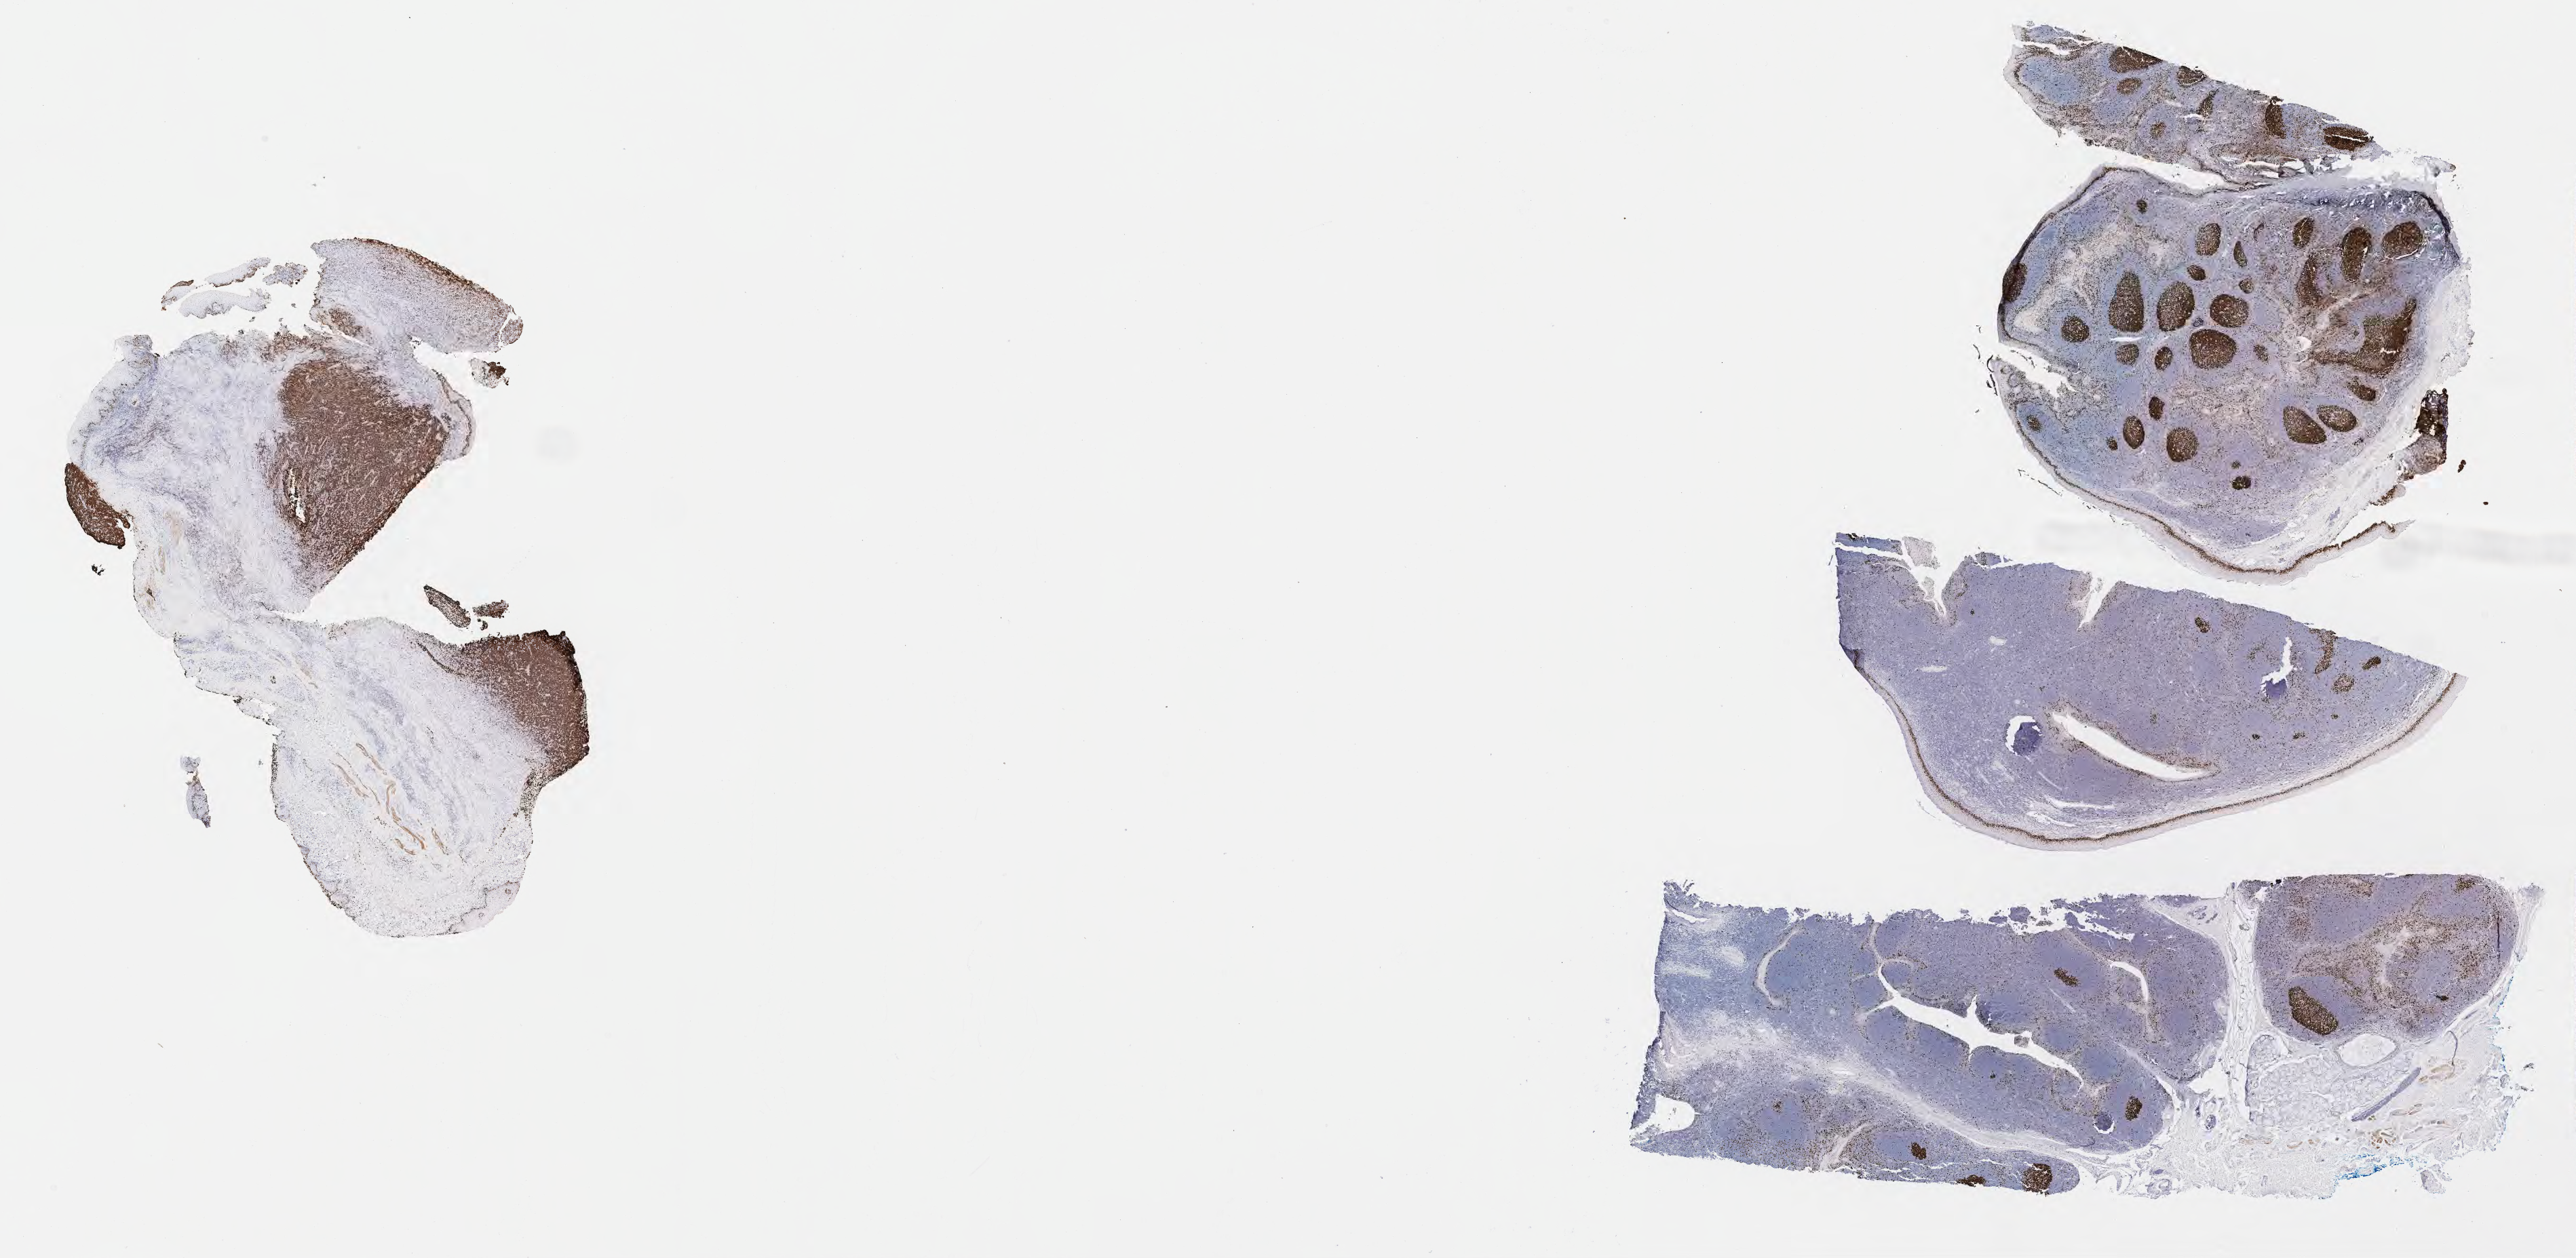
IHC for Ki-67, whole-slide image — whole scanned area (about 30.7 x 15.0 mm) shown as a low-resolution overview. Tumor tissue. Site: cranium. Patient male; age 10 years.
Diagnosis: Burkitt lymphoma, NOS.